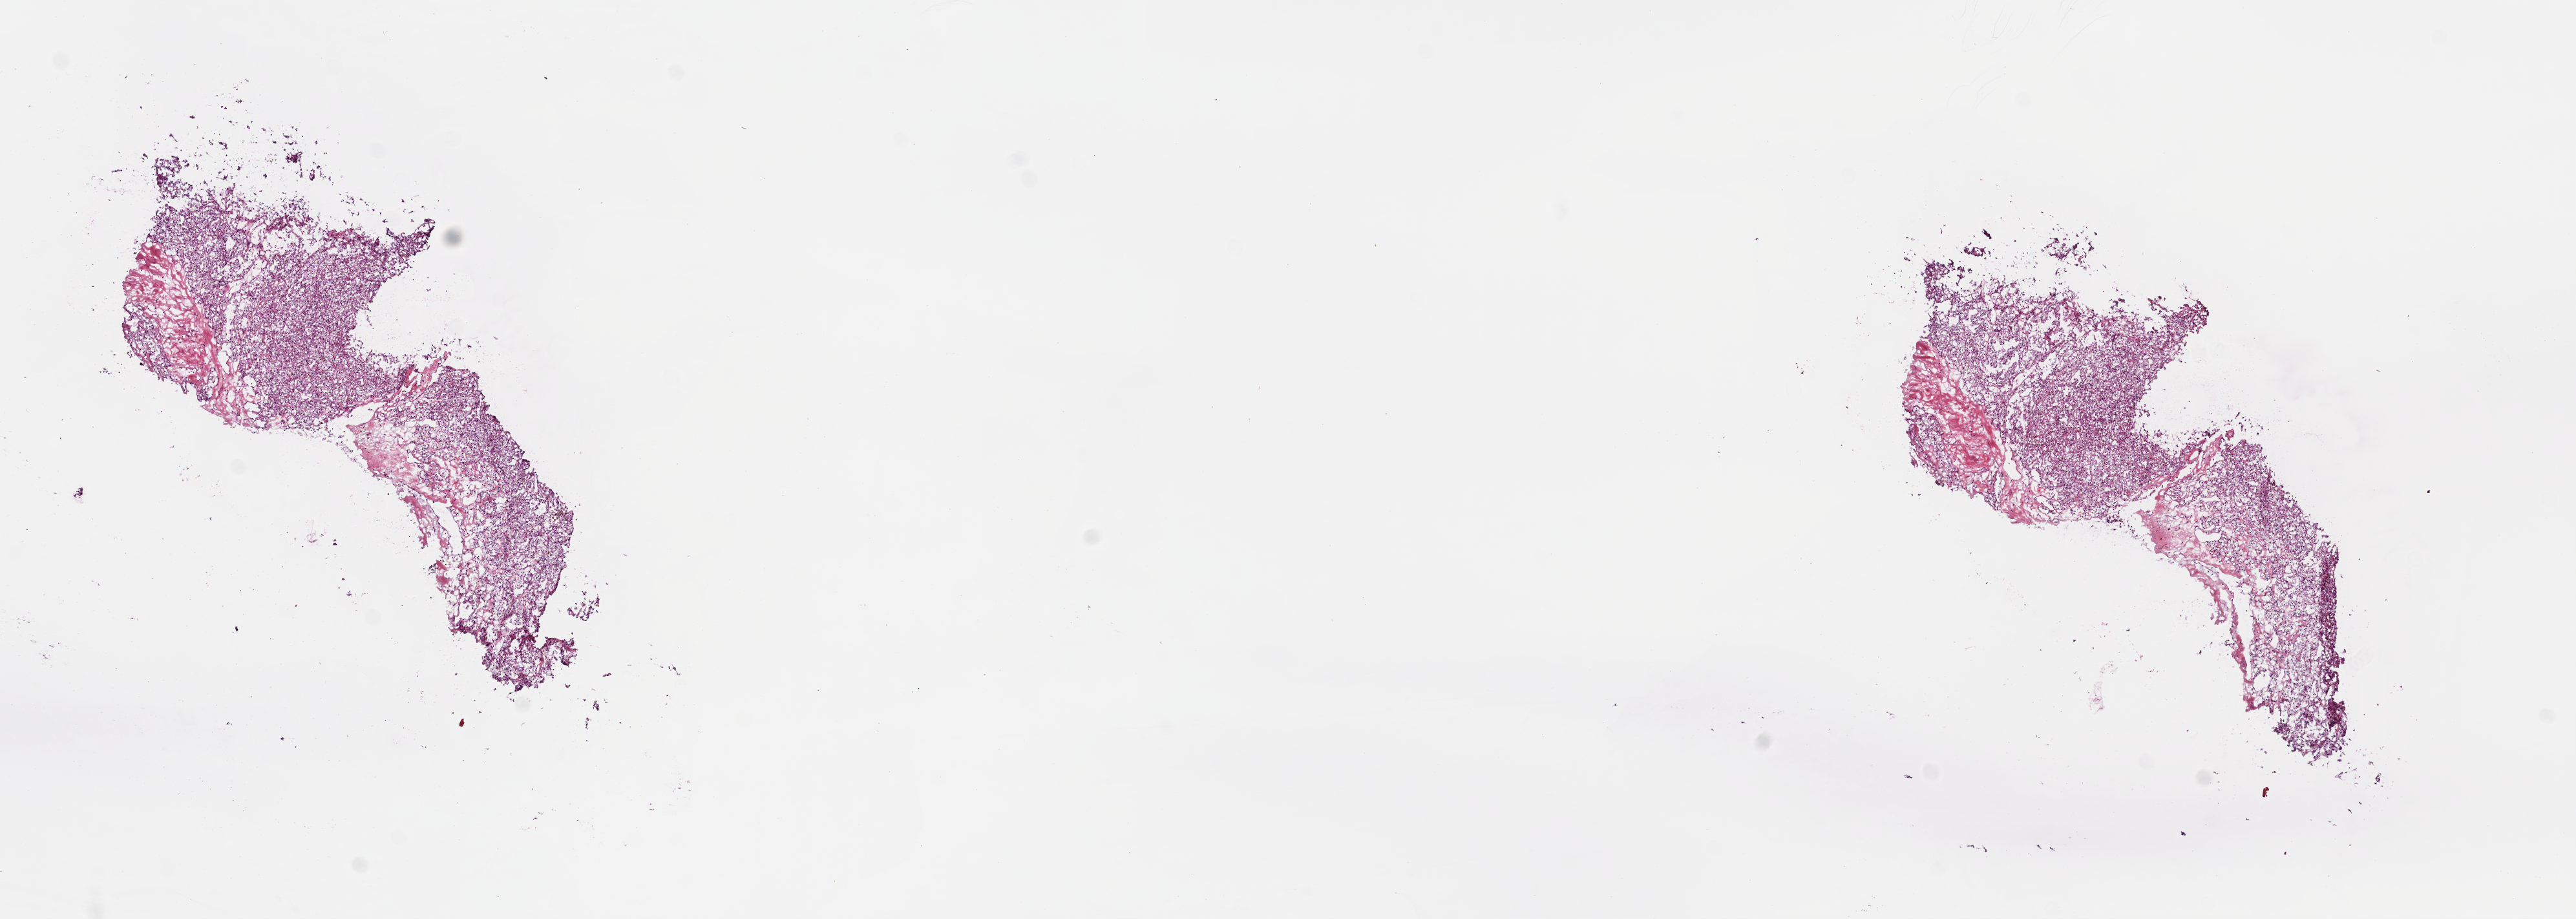
Whole-slide histology image, H&E-stained — low-resolution overview of the scanned area, about 15.7 x 5.6 mm (acquisition: 40x scan), frozen section, kidney, primary tumour sample. Patient: male, age at initial diagnosis 55 years. Histologic grade: G3 (poorly differentiated). Composition of this section per pathologist review: tumour cells 90%, tumour nuclei 90%, normal cells 0%, stromal cells 10%, necrosis 0%. Inflammatory infiltration, as recorded: lymphocyte infiltration 0%, monocyte infiltration 0%, neutrophil infiltration 0%.
* histologic diagnosis: Clear cell adenocarcinoma, NOS
* laterality: left
* AJCC pathologic stage: I